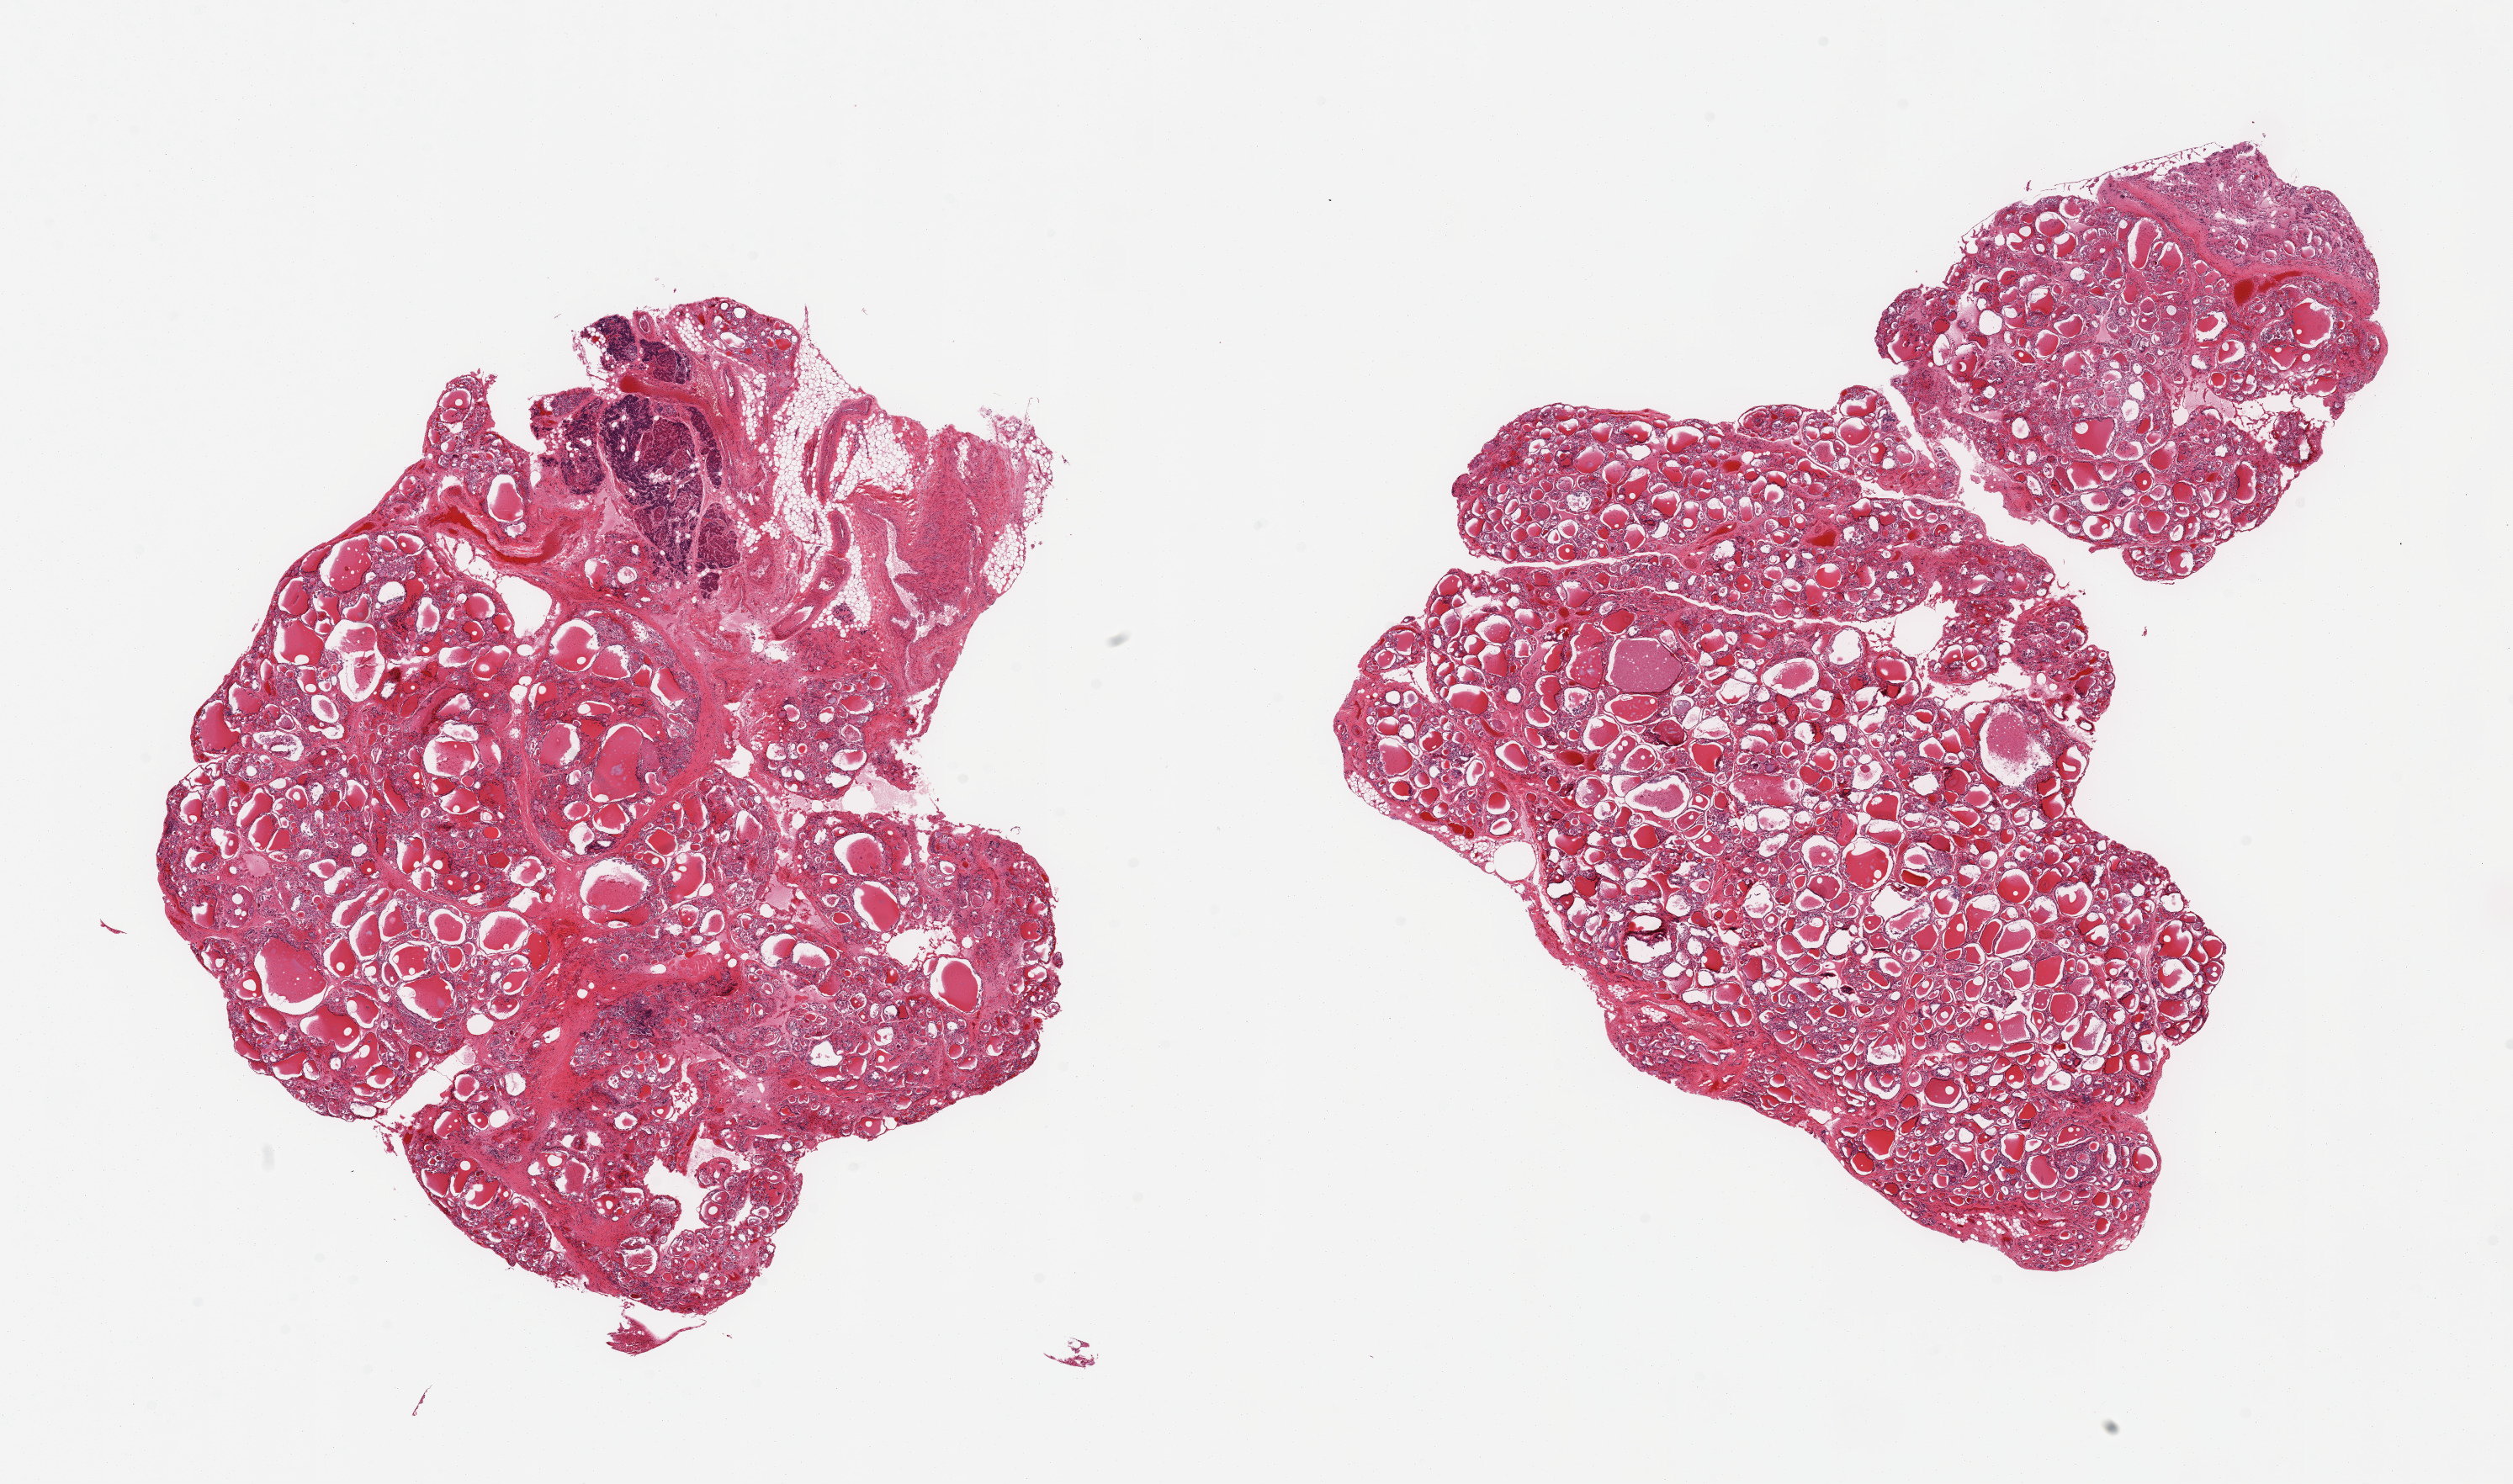
Digitized hematoxylin and eosin (H&E)-stained section, shown as a low-resolution overview of the whole scanned area (about 23.6 x 14.0 mm); PAXgene-fixed paraffin-embedded (PFPE) section; section of thyroid (target tissue); donor tissue sample. Donor sex: male.
- pathologist's review note for this sample: 2 pieces, nubbin of adherent fat/fibrous tissue; contains ~3mm parathyroid tissue